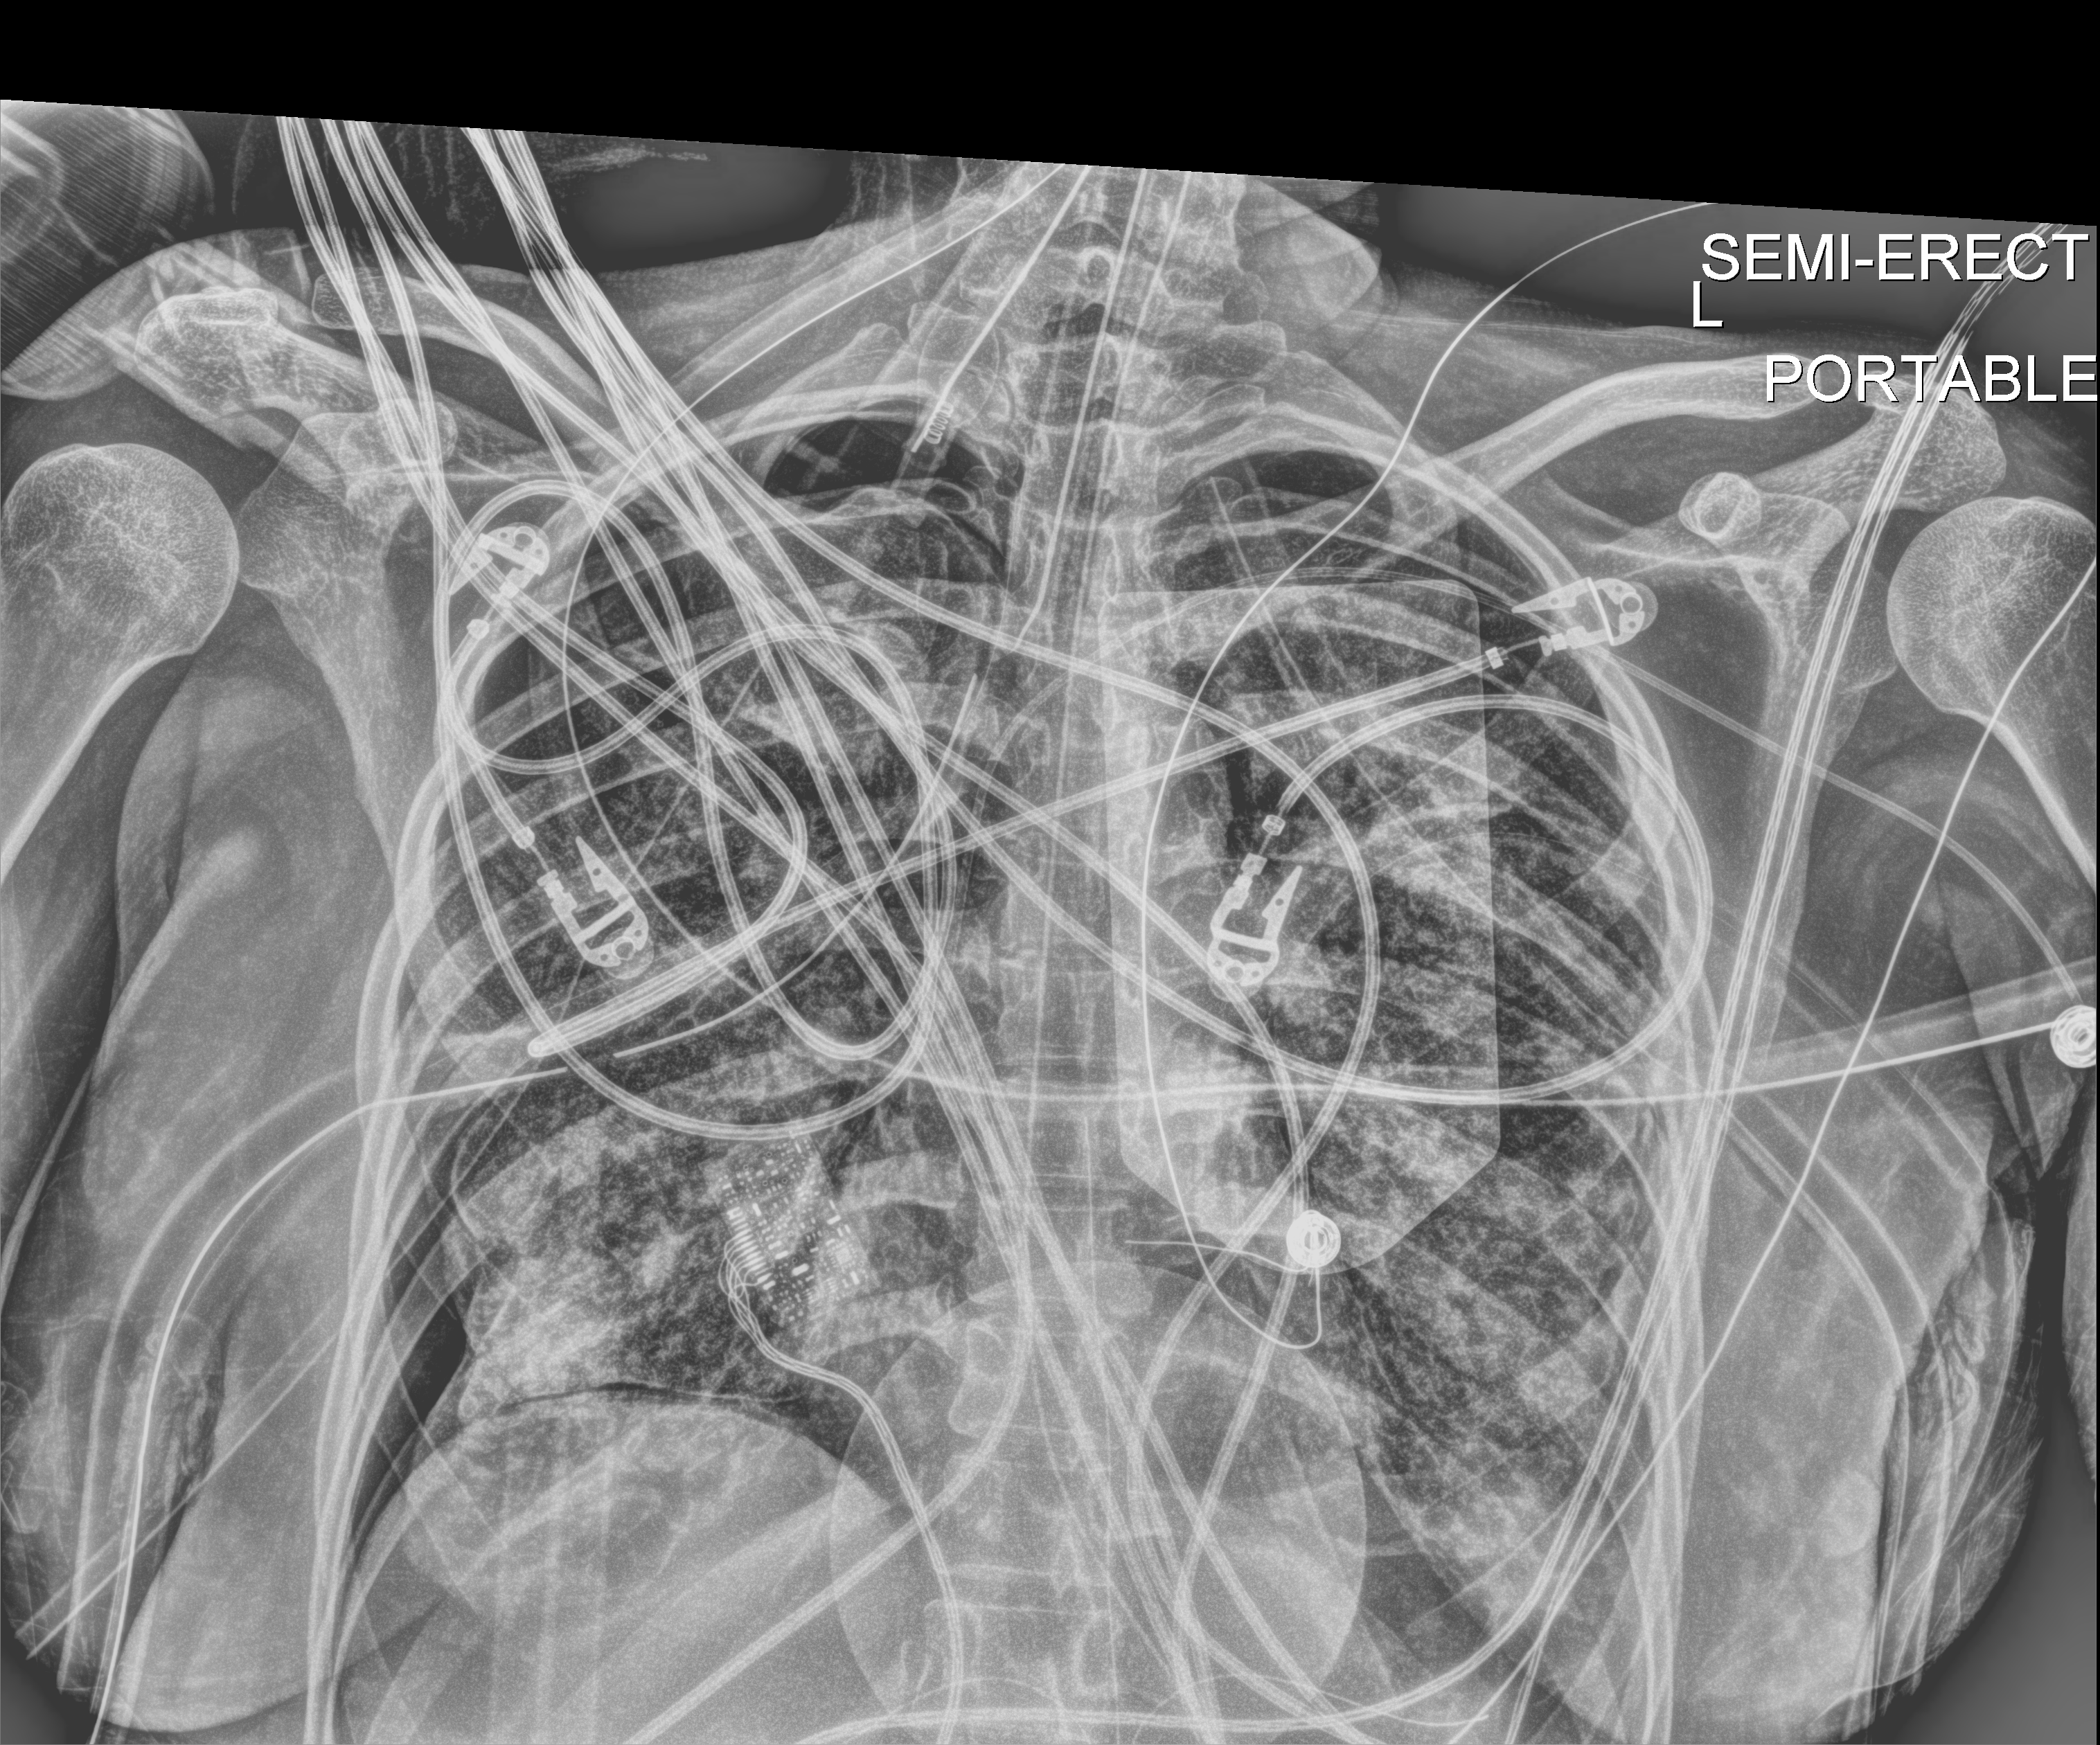
Bedside chest radiograph (digital radiography), anteroposterior (AP) projection. Patient hospitalised with COVID-19, aged 18–59 years.
Admission-level facts for this patient (not findings on this image; timing relative to this image not recorded):
- admitted to intensive care during this hospital stay: yes